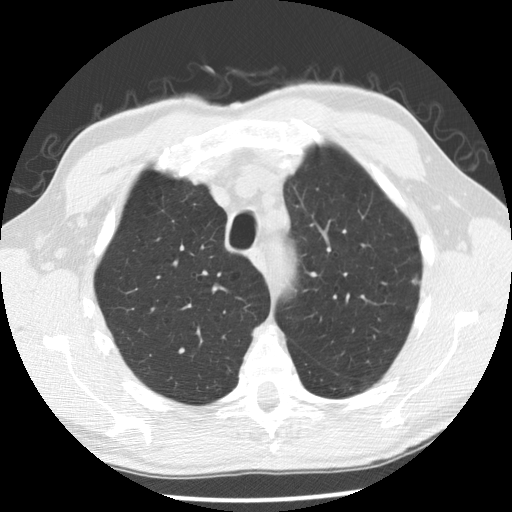
Chest CT (low-dose screening protocol), one axial image. Second annual screen. Lung window (W 1500 / L -600 HU). 2.5 mm slice thickness. Standard (soft-tissue) reconstruction kernel (STANDARD). 512 × 512 image matrix, field of view 340 × 340 mm. Male participant, aged 63 years at enrolment. Current smoker at enrolment.
Expert reader's lesion annotation, bounding box (x1, y1, x2, y2) in pixels: (398, 264, 433, 295). The exam's reader record, not a measurement of the box and not confirmed to be the same lesion: non-calcified nodule or mass ≥4 mm, left upper lobe, 5 × 3 mm, poorly defined margins, soft tissue attenuation, pre-existing on the prior screen: yes; interval growth: no. Official screen result: positive, no significant change: stable abnormalities potentially related to lung cancer, unchanged since the prior screening exam. Later outcome: lung cancer diagnosed 445 days after this screen (after the third annual screen) — adenocarcinoma, NOS, left upper lobe, well differentiated (G1), stage IB (AJCC 6th edition), 5 mm at pathology.